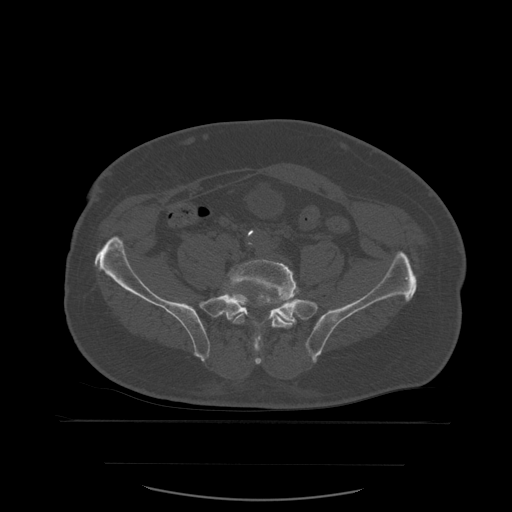
CT including the spine, one axial slice. Position 127 of 590 along the scan axis. Bone window (W 1800 / L 400 HU). 1.25 mm slice thickness. 512 × 512 image matrix, field of view 479 × 479 mm. Patient age 71 years. Case-level facts recorded for this patient, not image findings: primary cancer: lung; vertebrae with lytic lesions (as recorded): T1, T2, L5, S1.
Outlined on this slice (semi-automatically segmented with operator editing):
- L5 vertebra: bounding box <220,260,298,349> (left, top, right, bottom; pixels)